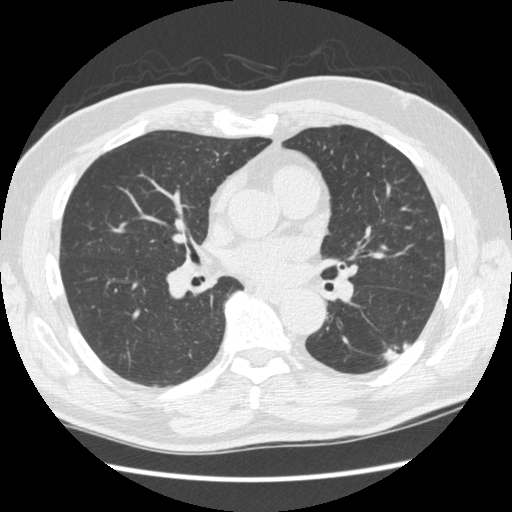
Axial slice from a low-dose chest CT screening exam; baseline screening round; lung window (W 1500 / L -600 HU); standard (soft-tissue) reconstruction kernel (STANDARD); 120 kVp; slice 127 of 267 in the series. Male, age 74 years at enrolment.
Lesion marked by an expert reader, bounding box [x1, y1, x2, y2] px = [375, 324, 417, 372]. The screening reader recorded 3 non-calcified nodules or masses ≥4 mm on this exam (right upper lobe, right lower lobe, left upper lobe); which of them this box marks is not recorded. Lung cancer was diagnosed 384 days after this screen: squamous cell carcinoma, NOS, left lower lobe, well differentiated (G1), stage IA (AJCC 6th edition), 28 mm at pathology.